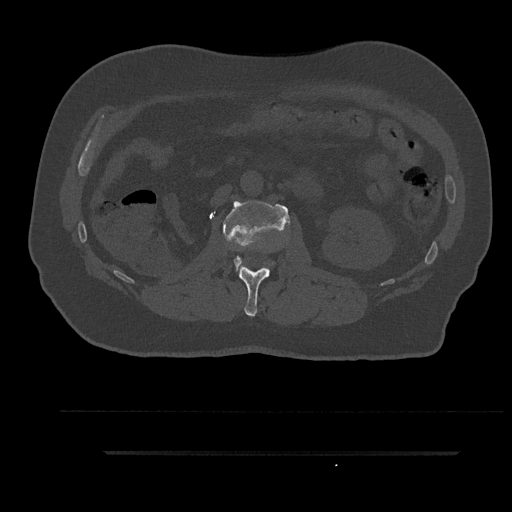
CT including the spine, one axial slice. Position 144 of 797 along the scan axis. 120 kVp. Bone window (W 1800 / L 400 HU). 0.5 mm slice thickness. 512 × 512 image matrix, field of view 432 × 432 mm. Patient: male, 63 years. From the clinical record (not read from this slice): primary cancer: renal; vertebrae with lytic lesions (as recorded): T8.
Structures marked on this image (semi-automatically segmented with operator editing):
- L1 vertebra: box from (x=237, y=251) to (x=270, y=316) px
- L2 vertebra: (x=223, y=201)–(x=290, y=268)